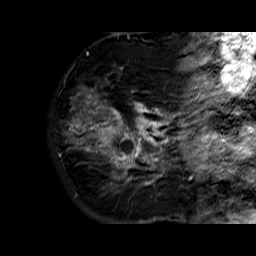
Breast MRI (dynamic contrast-enhanced), one sagittal slice. Position 17 of 60 along the scan axis. Dynamic contrast-enhanced series, time point 2 of 6 at this slice position (early post-contrast). 1.5 T. TE 6.3 ms, TR 32.4 ms. 4 mm slice thickness. 256 × 256 image matrix. Female patient. Case-level facts recorded for this patient, not image findings: setting: breast cancer imaged before/during neoadjuvant chemotherapy; receptor status: HR-positive, HER2-negative.
Outlined on this slice (semi-automatic segmentation, software-assisted and operator-edited):
- analysis volume of interest (the breast-tissue region the enhancement analysis was run in; not a lesion): bounding box (x1, y1, x2, y2) in pixels: (70, 73, 177, 183)
- tumour enhancement mask (voxels above the 100 % enhancement threshold inside the analysis volume of interest): (80, 96, 177, 183)